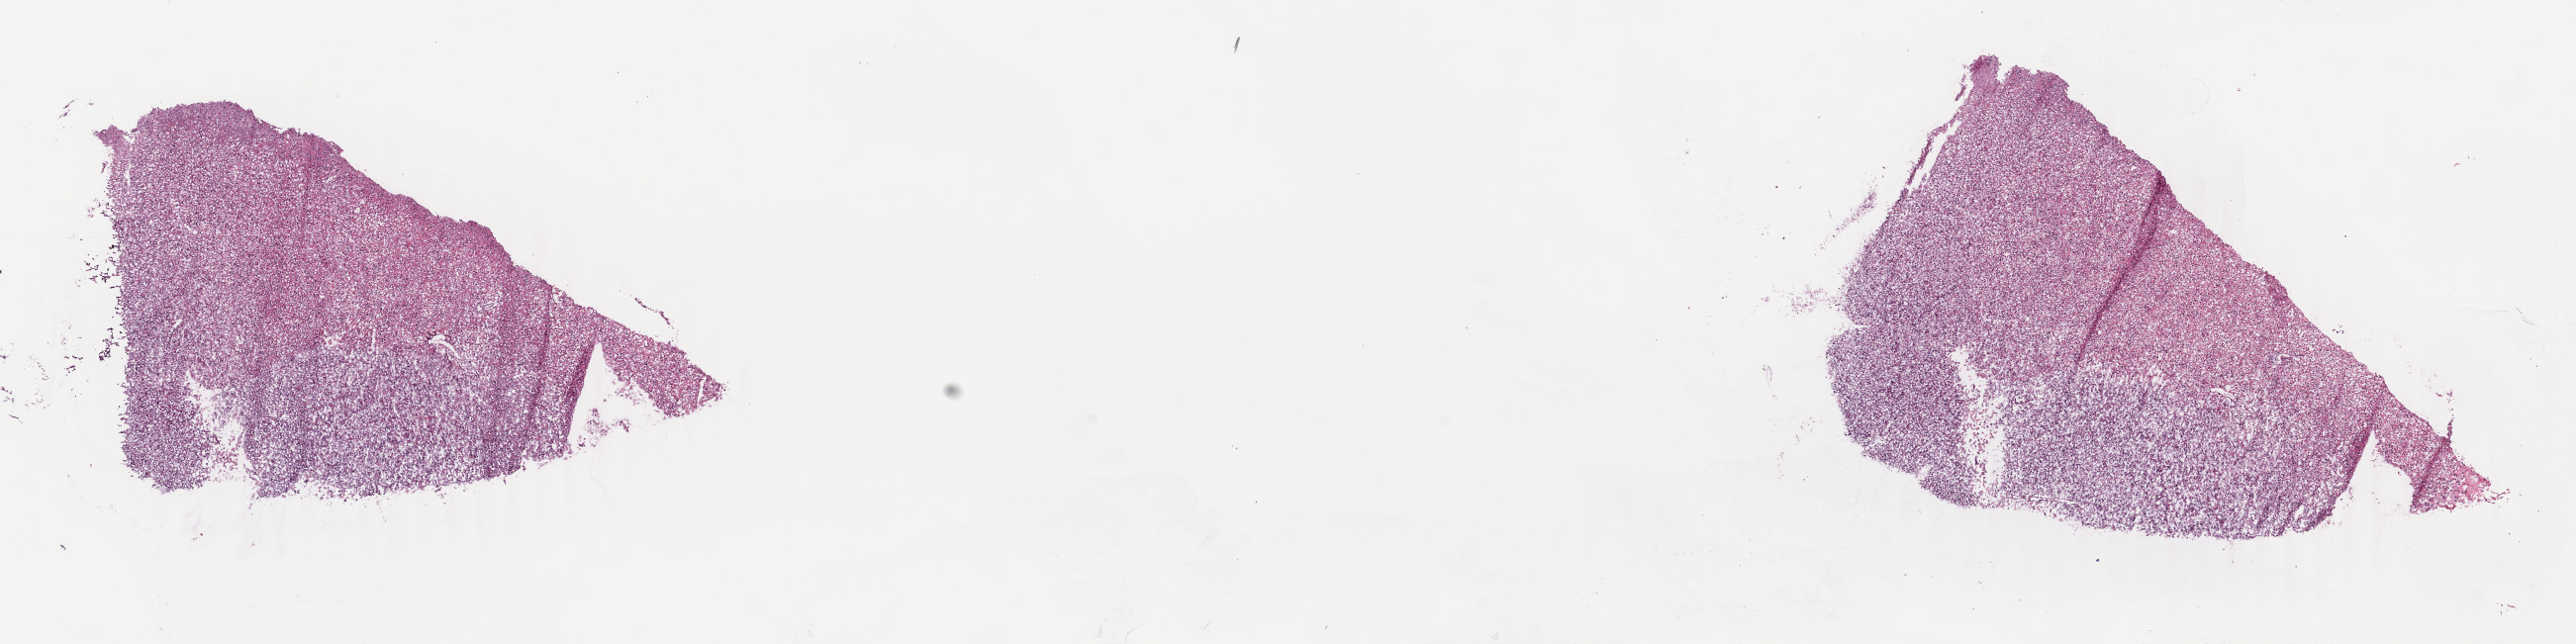
Hematoxylin and eosin (H&E) stained whole-slide image, whole scanned area (about 20.7 x 5.2 mm) shown as a low-resolution overview; frozen section; sample: primary tumour, brain. Male patient; age at initial diagnosis 54 years.
Pathologic diagnosis: Oligodendroglioma, NOS.